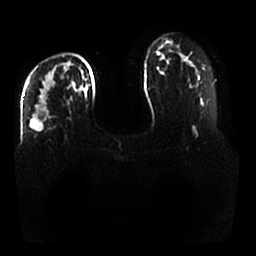
Breast MRI, one axial slice. Slice 18 of 25 in the series (ordered by position). Diffusion-weighted series; image 2 of 4 stored at this slice position (different b-values; order by instance number). 1.5 T. 4 mm slice thickness. 256 × 256 image matrix. Female patient.
Structures marked on this image (expert manual segmentation):
- tumour on diffusion-weighted imaging: box from (x=31, y=61) to (x=72, y=132) px